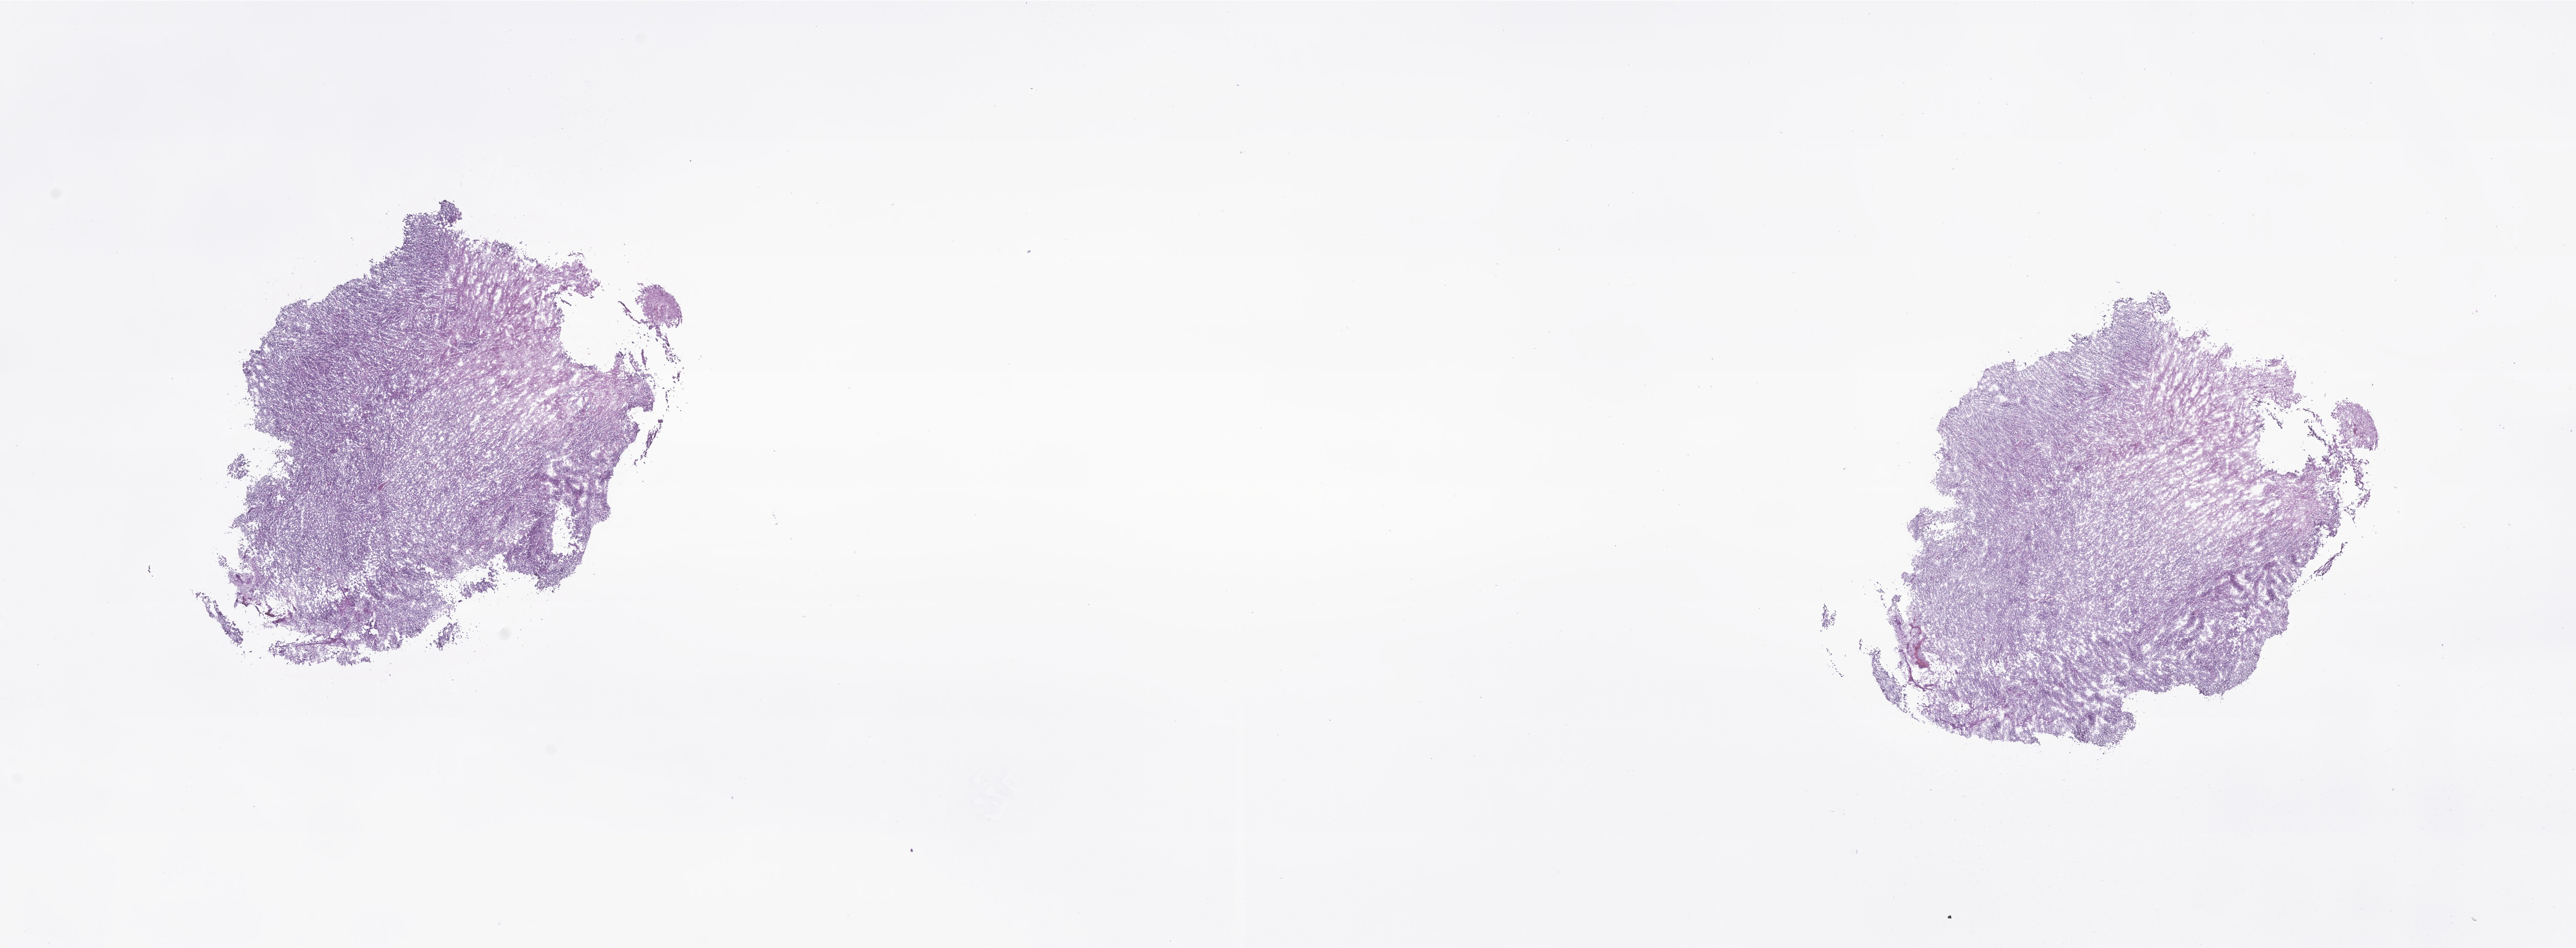
Digitized H&E-stained section of tumor tissue from the brain — low-resolution overview of the scanned area, about 23.8 x 8.8 mm. Cryosection (OCT / tissue freezing medium). Patient male; age 53 months (4 years 5 months).
• recorded diagnosis: CNS embryonal tumor, NOS